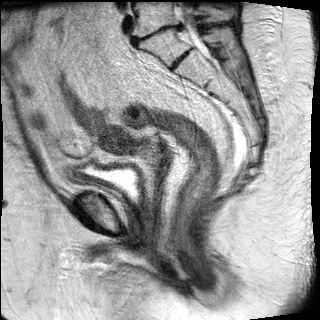
Pelvic MRI for cervical cancer, one sagittal slice; position 15 of 27 along the scan axis; T2-weighted; 1.5 T; TE 89 ms, TR 2740 ms; 4 mm slice thickness; 320 × 320 image matrix, field of view 260 × 260 mm. Patient: female, 67 years.
Annotated regions visible in this slice (expert manual segmentation):
- uterus and cervix: bounding box <99,124,136,156> (left, top, right, bottom; pixels)